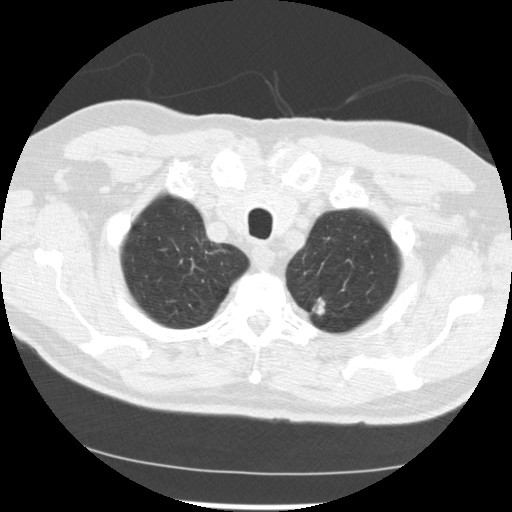
Low-dose screening chest CT, one axial slice. Slice 219 of 249 in the series (ordered by position). Reconstruction kernel STANDARD. Lung window (W 1500 / L -600 HU). 2.5 mm slice thickness. 512 × 512 image matrix, field of view 341 × 341 mm.
Annotated regions visible in this slice (expert manual segmentation):
- lesion 2 (tumor, upper lobe of left lung): box from (x=314, y=298) to (x=325, y=314) px